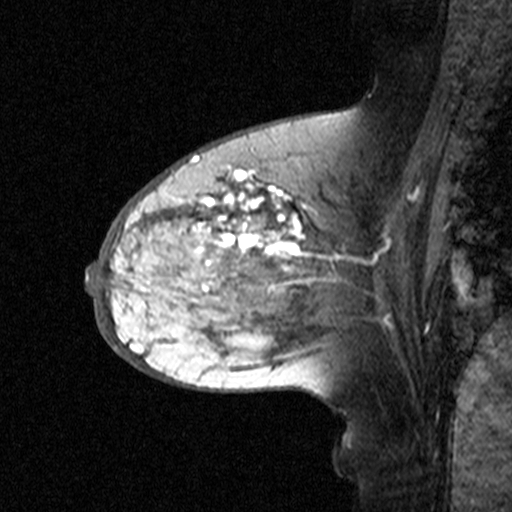
Breast MRI (dynamic contrast-enhanced), one sagittal slice. Slice 23 of 44 in the series (ordered by position). Dynamic contrast-enhanced study with each time point stored as its own series, time point 2 of 3 at this slice position (early post-contrast, ordered by acquisition time). 1.5 T. TE 4.5 ms, TR 11 ms. 3 mm slice thickness. 512 × 512 image matrix. Female patient, age 65 years. From the clinical record (not read from this slice): setting: breast cancer imaged before/during neoadjuvant chemotherapy; receptor status: HER2-positive.
Structures marked on this image (semi-automatically segmented with operator editing):
- analysis volume of interest (the breast-tissue region the enhancement analysis was run in; not a lesion): bounding box (x1, y1, x2, y2) in pixels: (160, 172, 329, 345)
- tumour enhancement mask (voxels above the 90 % enhancement threshold inside the analysis volume of interest): (188, 172, 304, 286)